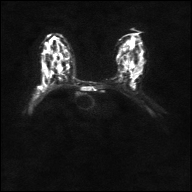
Breast MRI, one axial slice. Position 21 of 36 along the scan axis. Diffusion-weighted series; image 2 of 4 stored at this slice position (different b-values; order by instance number). 1.5 T. 192 × 192 image matrix, field of view 360 × 360 mm. Female patient.
Structures marked on this image (outlined manually by an expert reader):
- tumour on diffusion-weighted imaging: bounding box <39,86,43,89> (left, top, right, bottom; pixels)